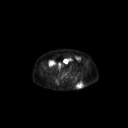
FDG PET of an extremity soft-tissue mass (from a PET/CT study), one axial slice. Position 76 of 267 along the scan axis. 3.27 mm slice thickness. 128 × 128 image matrix, field of view 700 × 700 mm. Male patient, age 69 years. From the clinical record (not read from this slice): histological type: leiomyosarcoma; grade: intermediate; site of the primary tumour: left pelvis.
Structures marked on this image (expert contour drawn on MRI and transferred to this co-registered scan by the dataset authors):
- gross tumour volume (mass): bounding box (x1, y1, x2, y2) in pixels: (76, 82, 83, 89)